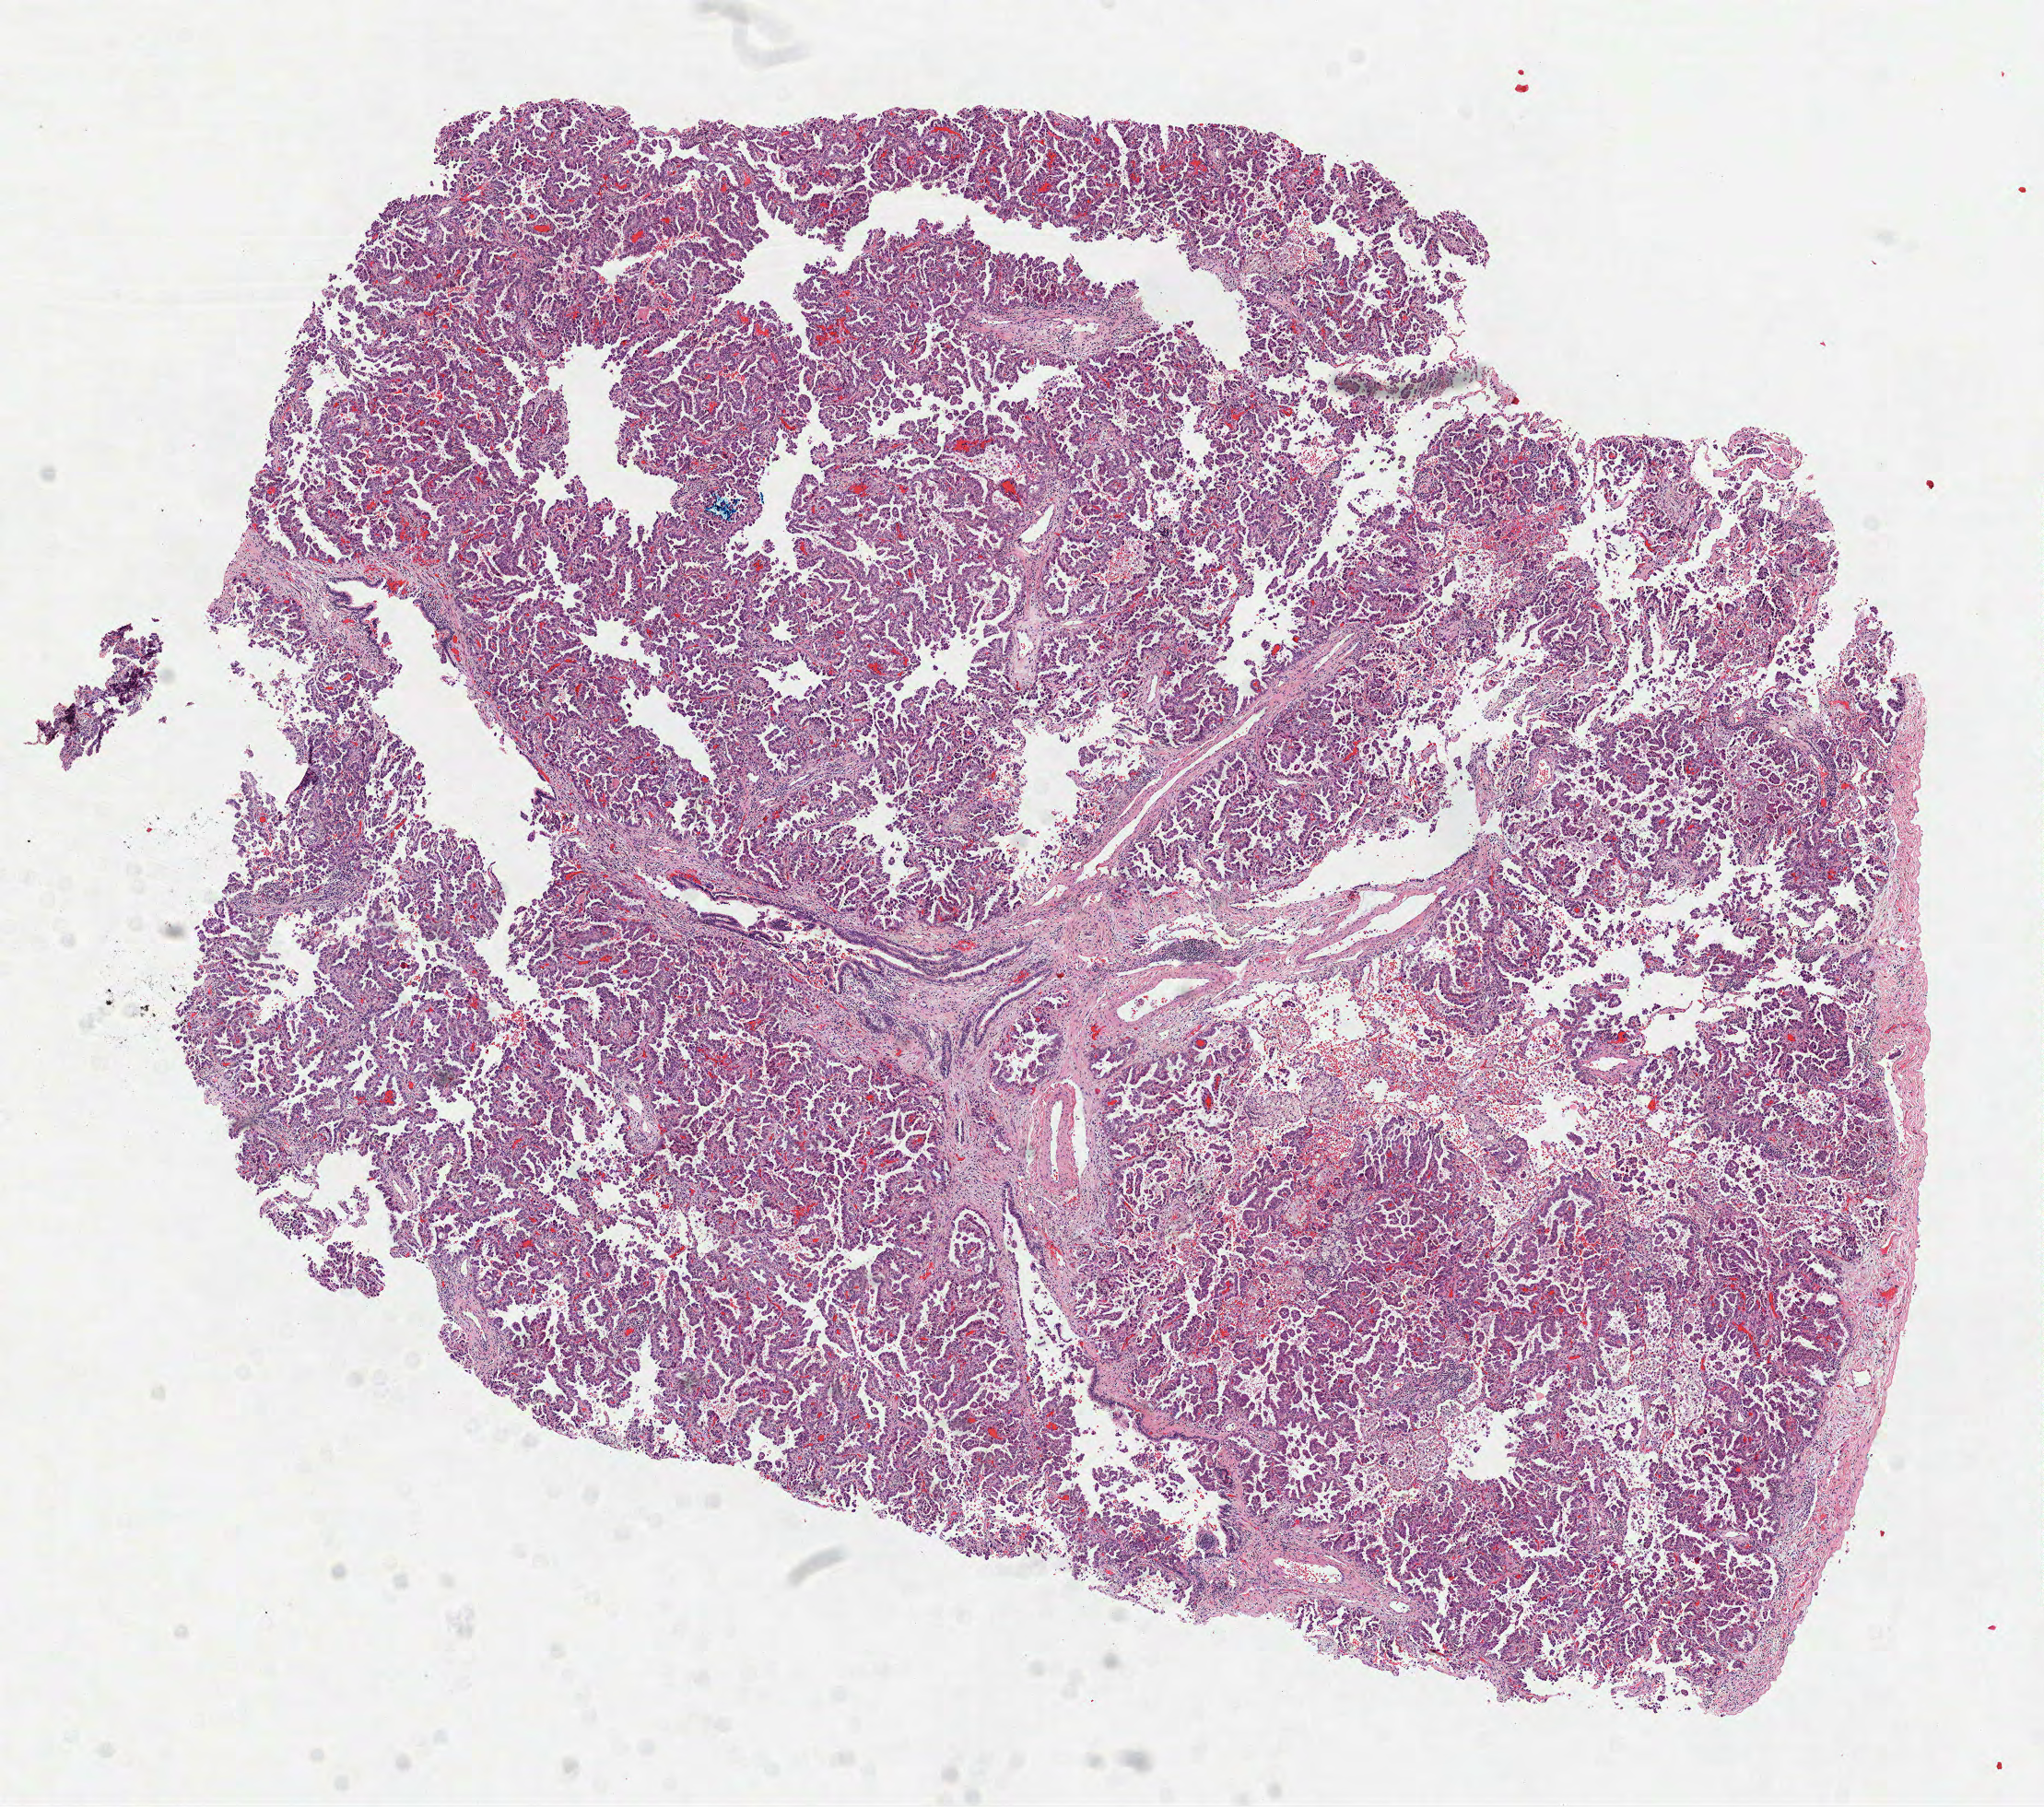
H&E-stained whole-slide image, low-resolution overview of the scanned area, about 8.9 x 7.9 mm, frozen section from the top of the tissue portion, primary tumour sample from the lung. Female, age 52 years at initial diagnosis. Composition of this section per pathologist review: tumour cells 85%, tumour nuclei 80%, normal cells 0%, stromal cells 15%, necrosis 0%.
* AJCC pathologic stage: IB (7th edition)
* laterality: right
* histologic diagnosis: Adenocarcinoma, NOS (lower lobe, lung)
* TNM: T2a N0 M0